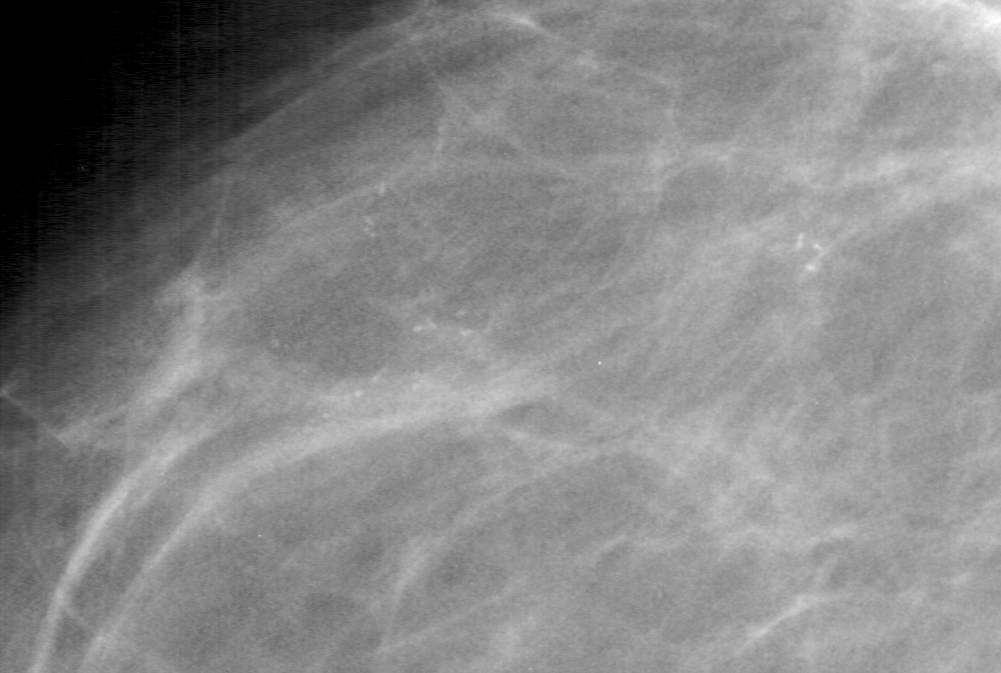
Cropped region of a digitized screen-film mammogram centred on a radiologist-marked abnormality, left breast, MLO view, BI-RADS breast density category 3 (scale 1–4).
Finding: calcifications, morphology pleomorphic, distribution linear; BI-RADS assessment category 5; pathology result (as recorded, not read from the image): malignant.